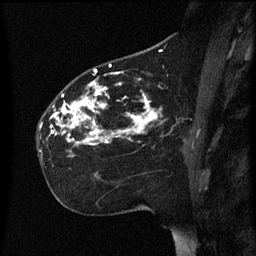
Breast MRI (dynamic contrast-enhanced), one sagittal slice; slice 36 of 60 in the series (ordered by position); dynamic contrast-enhanced series, image 2 of 3 at this slice position (ordered by acquisition); 1.5 T; TE 4.2 ms, TR 8.4 ms; 2.2 mm slice thickness; 256 × 256 image matrix. Patient: female, 35 years. From the clinical record (not read from this slice): setting: breast cancer imaged before/during neoadjuvant chemotherapy; receptor status: HER2-positive.
Structures marked on this image (semi-automatic segmentation, software-assisted and operator-edited):
- analysis volume of interest (the breast-tissue region the enhancement analysis was run in; not a lesion): box from (x=38, y=78) to (x=173, y=161) px
- tumour enhancement mask (voxels above the 70 % enhancement threshold inside the analysis volume of interest): (x=52, y=80)–(x=159, y=145)